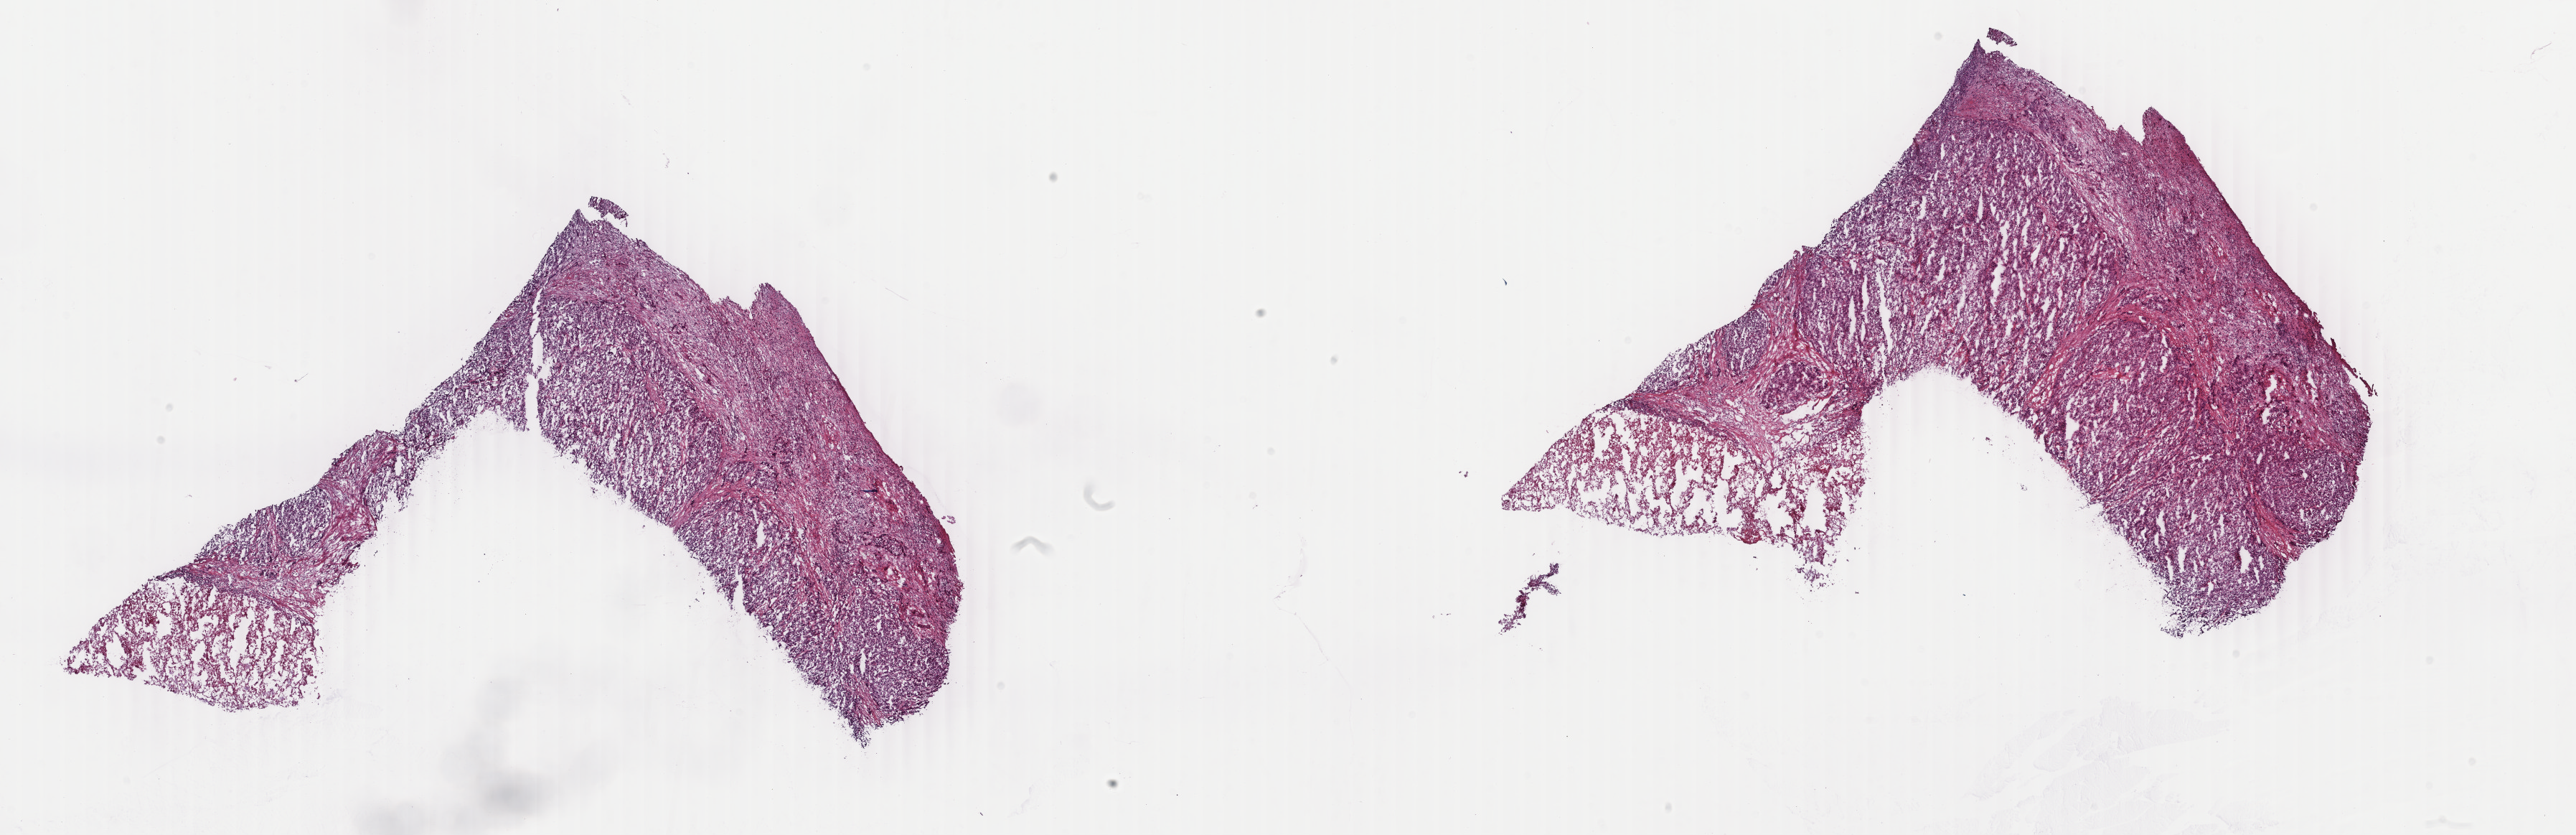
Whole-slide histology image, Hematoxylin and eosin (H&E) stained, shown as a low-resolution overview of the whole scanned area (about 28.6 x 9.3 mm, slide scanned at 40x). Frozen section from the top of the tissue portion. Sample: primary tumour, liver. Patient: female, age at initial diagnosis 58 years. Histologic grade: G2 (moderately differentiated). Slide review estimates, as recorded: tumour cells 100%, tumour nuclei 60%, normal cells 0%, stromal cells 0%, necrosis 0%. Infiltration values recorded for this section: lymphocyte infiltration 13%, monocyte infiltration 0%, neutrophil infiltration 0%.
AJCC pathologic stage: IIIB (6th edition). Pathologic diagnosis: Hepatocellular carcinoma, NOS.